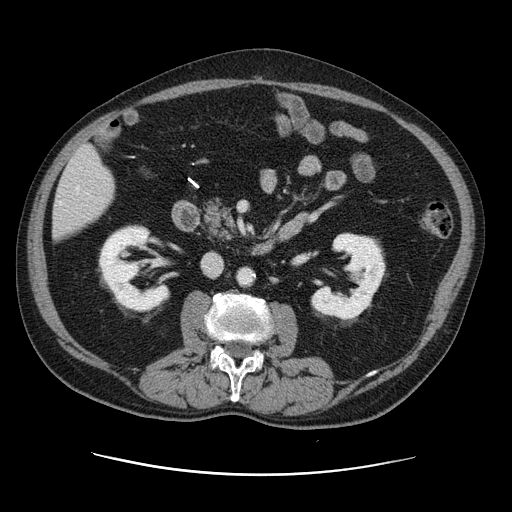
Contrast-enhanced abdominal CT, one axial slice. 120 kVp. Intravenous contrast given. Soft-tissue window (W 400 / L 40 HU). 2.5 mm slice thickness. 512 × 512 image matrix, field of view 395 × 395 mm. Male patient, age 72 years. Case-level facts recorded for this patient, not image findings: diagnosis: colorectal cancer liver metastases, imaged before liver resection; multiple liver metastases: yes; largest metastasis: 5.4 cm; disease in both lobes: yes.
Annotated regions visible in this slice (expert manual segmentation):
- hepatic veins: bounding box <60,187,79,204> (left, top, right, bottom; pixels)
- liver: <54,147,114,239>
- planned liver remnant (the part of the liver to remain after resection): <54,149,115,240>